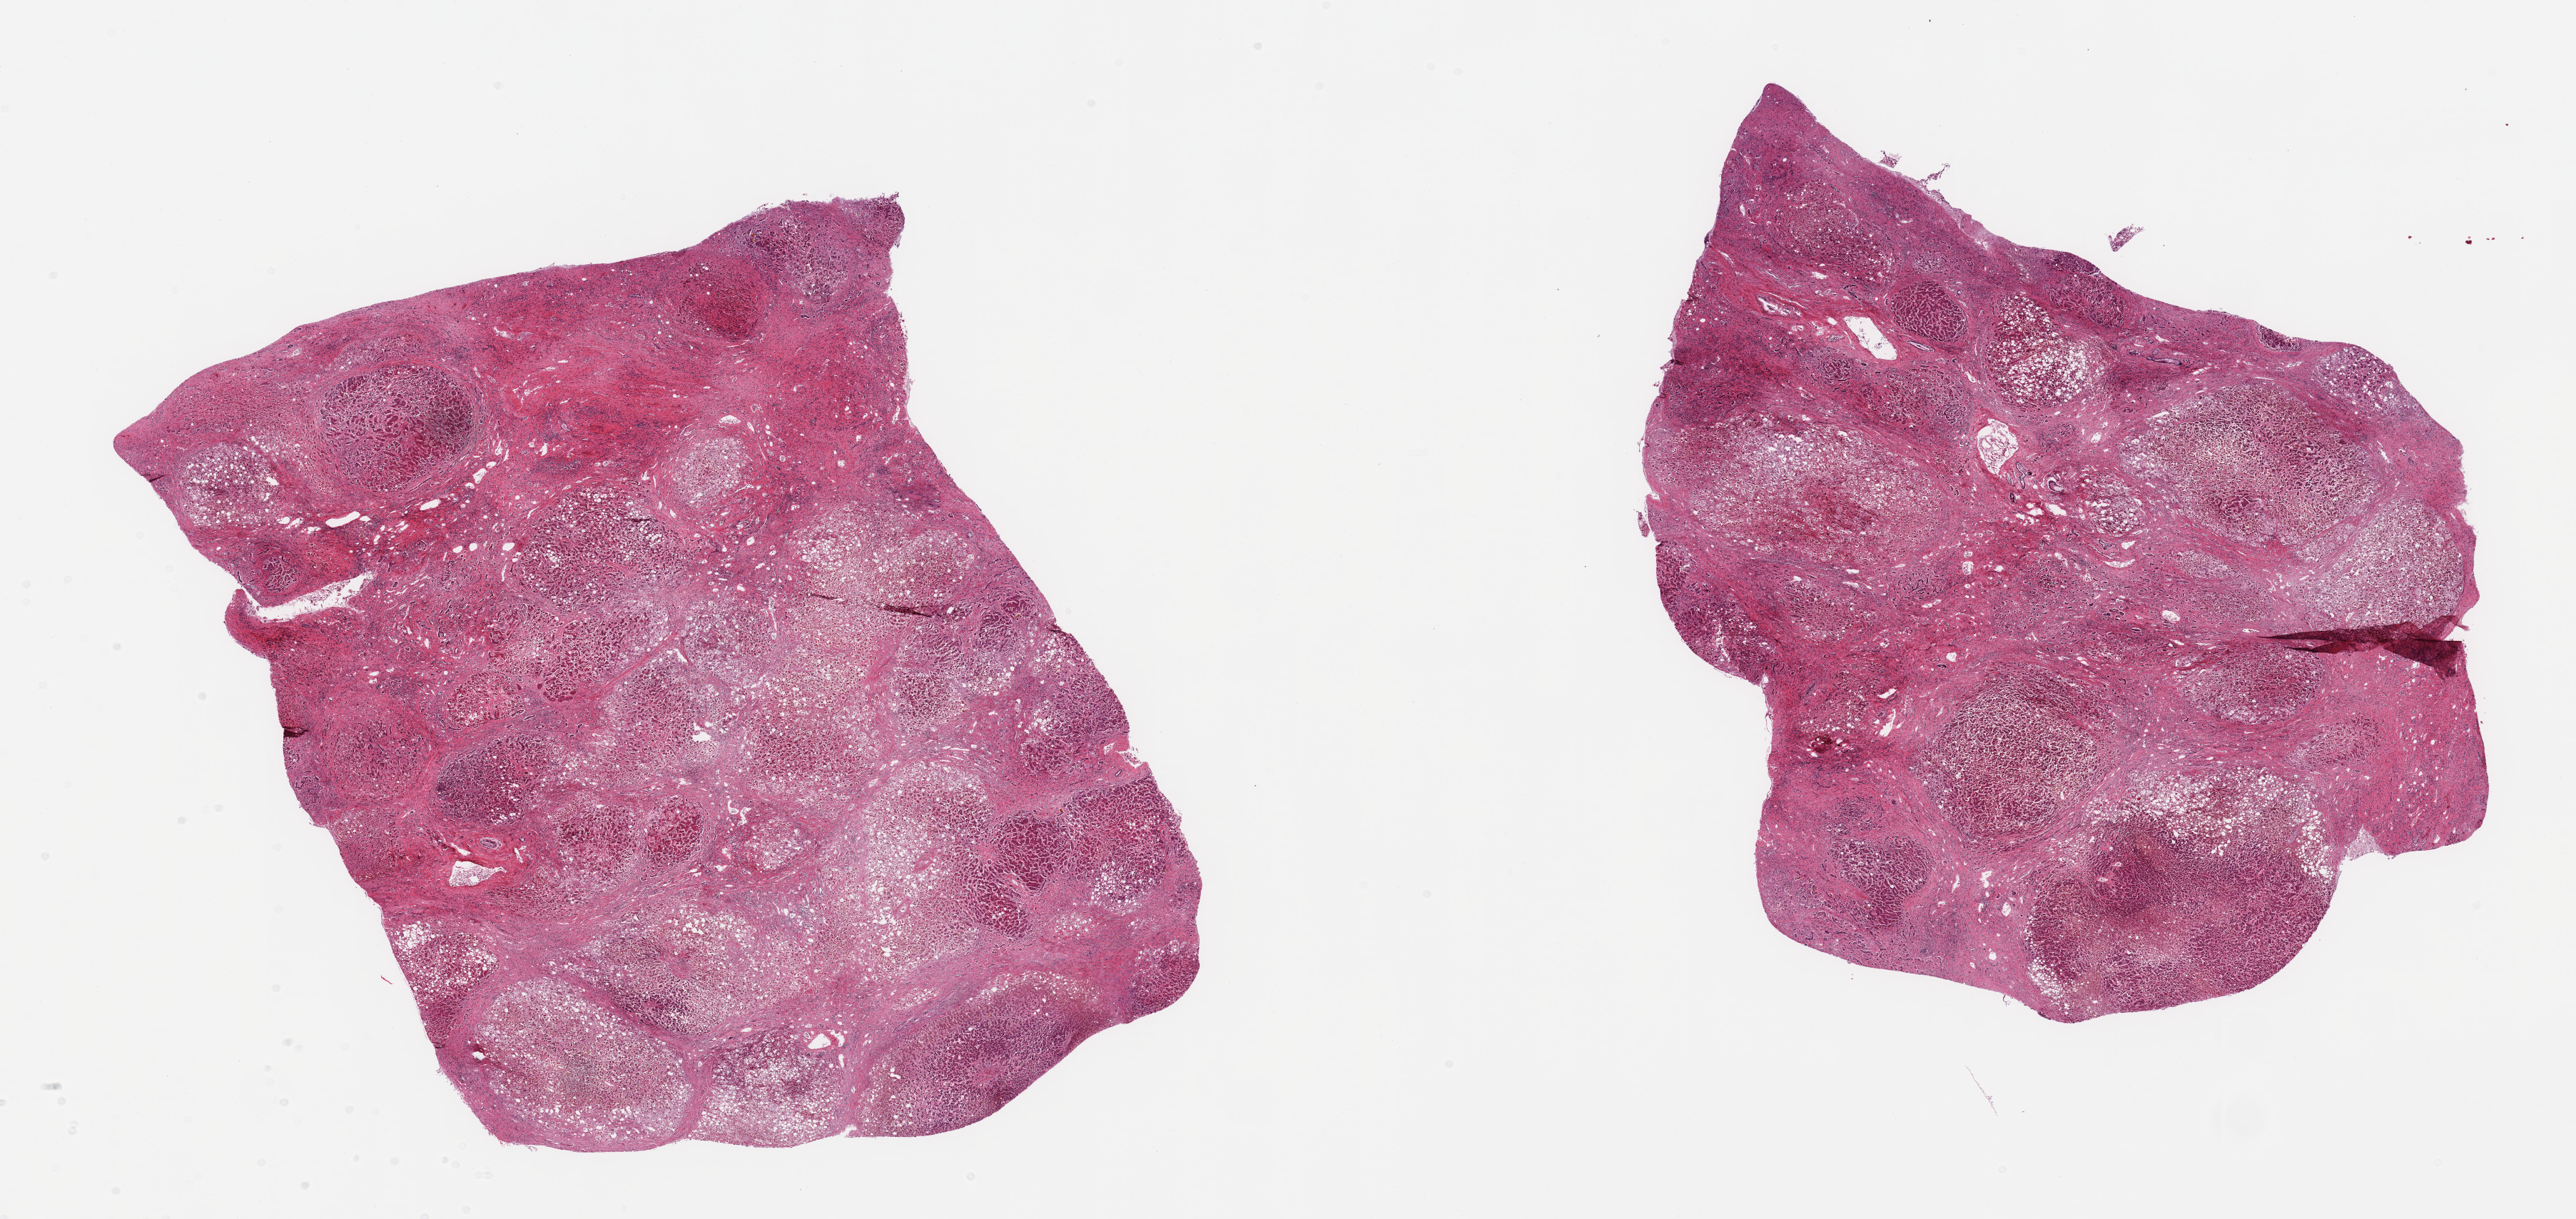
H&E whole-slide image — whole scanned area (about 28.5 x 13.5 mm) shown as a low-resolution overview, PAXgene-fixed, paraffin-embedded tissue, sampled site (target tissue): liver, tissue donor sample. Donor sex: male.
Pathologist's review note for this sample: 2 pieces, advanced autolysis. Established cirrhosis with diffuse macrovesicular steatosis.